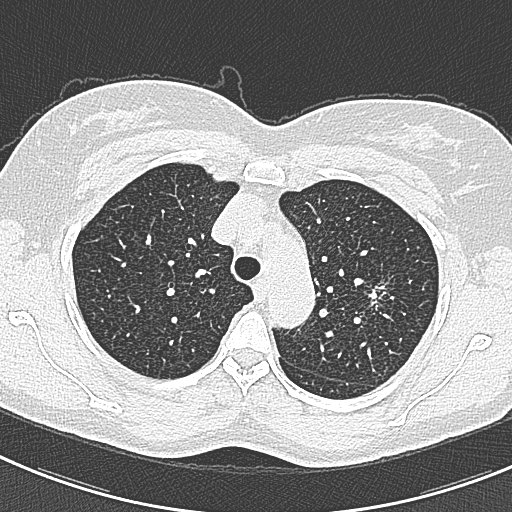
Axial slice from a low-dose chest CT screening exam. Baseline screening round. Lung window (W 1500 / L -600 HU). Lung (sharp) reconstruction kernel (B80f). 120 kVp. 512 × 512 image matrix, field of view 302 × 302 mm. Female, age 57 years at enrolment. Current smoker at enrolment.
Expert reader's lesion annotation, bounding box (x1, y1, x2, y2) in pixels: (362, 269, 412, 323). The screening reader recorded 2 non-calcified nodules or masses ≥4 mm on this exam (right lower lobe, left upper lobe); which of them this box marks is not recorded. Official screen result: positive, change unspecified: nodule(s) >= 4 mm or enlarging nodule(s), mass(es), or other non-specific abnormalities suspicious for lung cancer. Lung cancer was diagnosed 198 days after this screen: adenocarcinoma, NOS, left upper lobe, well differentiated (G1), stage IA (AJCC 6th edition), 10 mm at pathology.